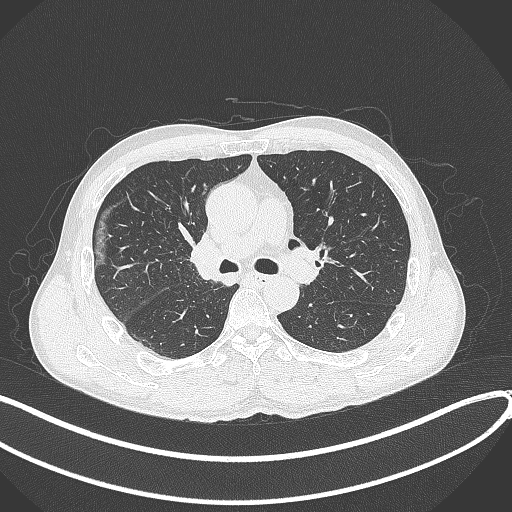
Chest CT, one axial slice. Reconstruction kernel B70f. Lung window (W 1500 / L -600 HU). 1 mm slice thickness. 512 × 512 image matrix, field of view 400 × 400 mm. Male patient, age 53 years. From the clinical record (not read from this slice): clinical TNM (as recorded): T1b N0 M0.
Structures marked on this image (rectangle marked by the reading radiologist):
- lung tumour (recorded histology: squamous cell carcinoma): bounding box <187,232,228,284> (left, top, right, bottom; pixels)